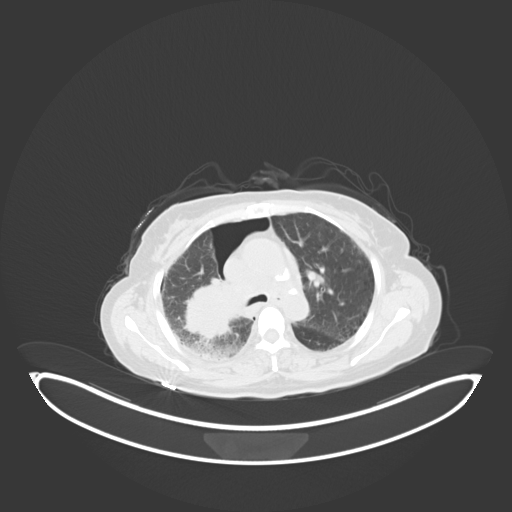
Chest CT, one axial slice. Slice 39 of 69 in the series (ordered by position). Reconstruction kernel B30f. 120 kVp. Lung window (W 1500 / L -600 HU). 3 mm slice thickness. 512 × 512 image matrix, field of view 500 × 500 mm. Female patient, age 64 years. Case-level facts recorded for this patient, not image findings: clinical TNM (as recorded): T3 N3 M0.
Outlined on this slice (rectangle marked by the reading radiologist):
- lung tumour (recorded histology: squamous cell carcinoma): bounding box [x1, y1, x2, y2] px = [183, 278, 233, 347]